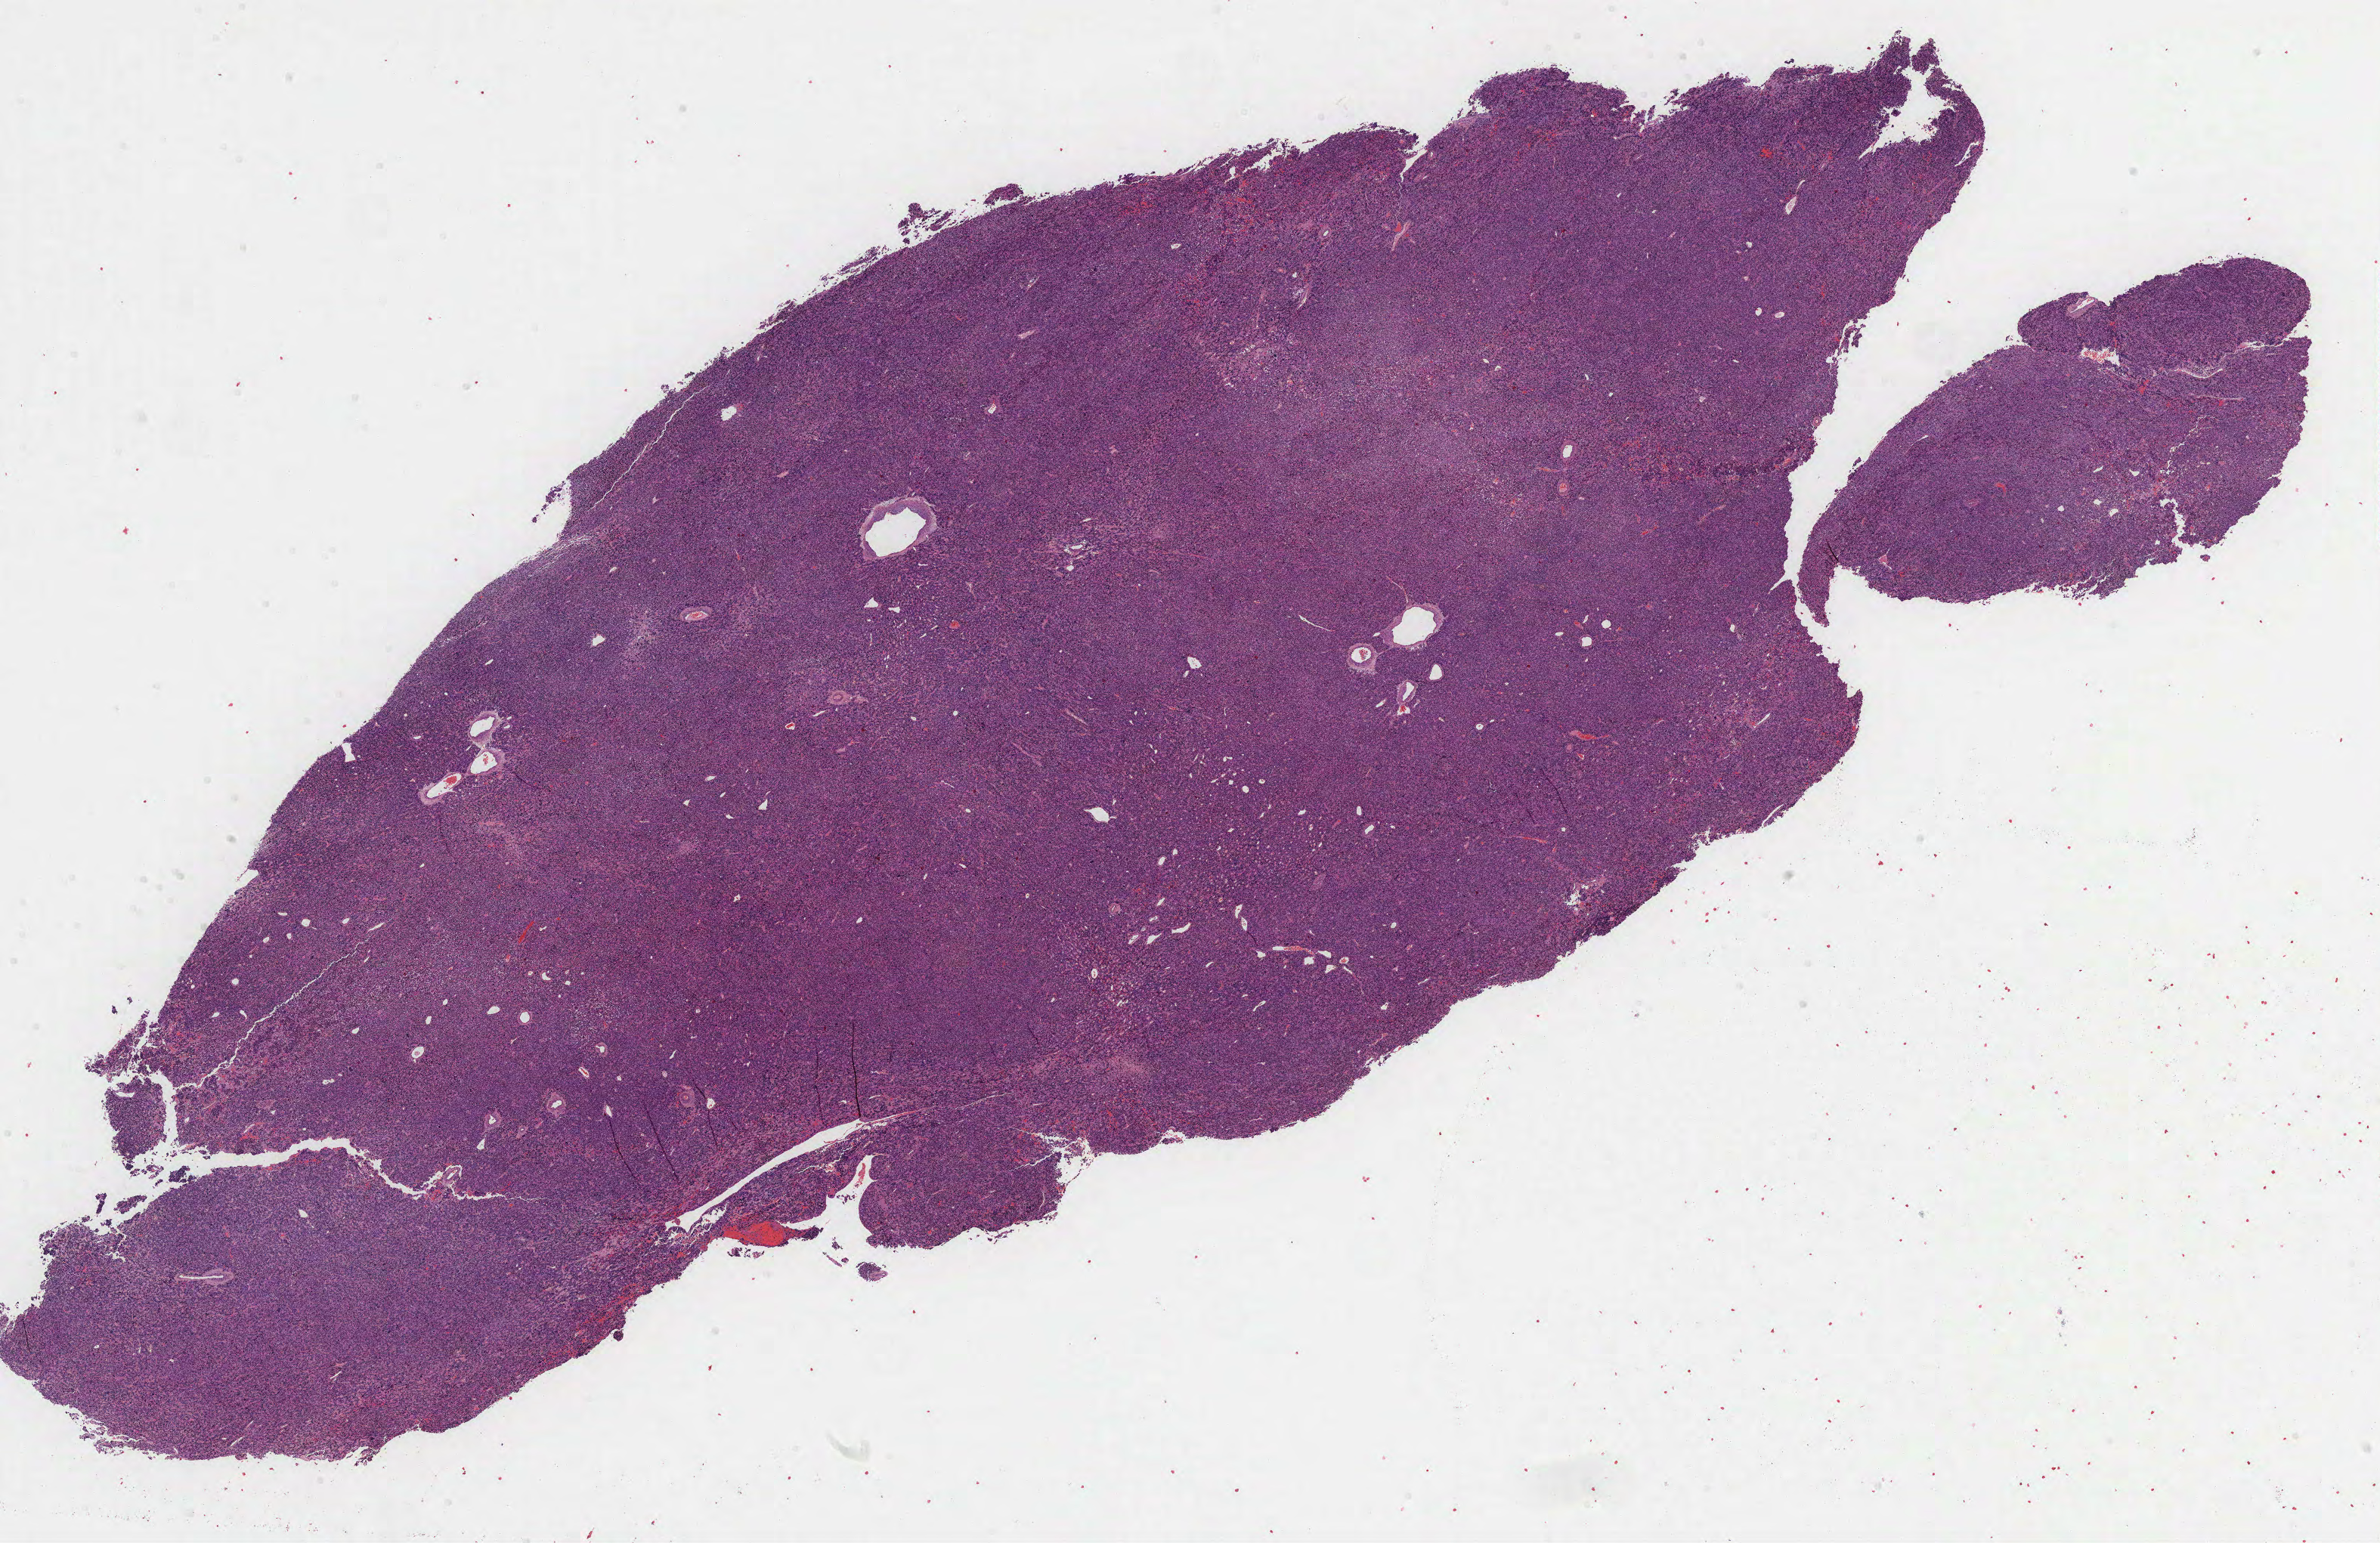
H&E-stained whole-slide image, shown as a low-resolution overview of the whole scanned area (about 25.4 x 16.5 mm), formalin-fixed paraffin-embedded (FFPE) diagnostic section, uterus, primary tumour sample. Patient: female, age at initial diagnosis 56 years.
Diagnosis: Leiomyosarcoma, NOS.